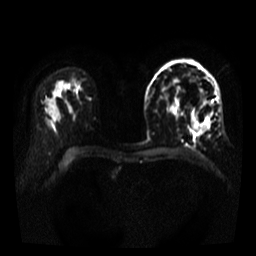
Breast MRI, one axial slice. Slice 23 of 35 in the series (ordered by position). Diffusion-weighted series; image 2 of 4 stored at this slice position (different b-values; order by instance number). 3 T. 5 mm slice thickness. 256 × 256 image matrix, field of view 320 × 320 mm. Female patient.
Outlined on this slice (expert manual segmentation):
- tumour on diffusion-weighted imaging: bounding box [x1, y1, x2, y2] px = [191, 113, 211, 132]